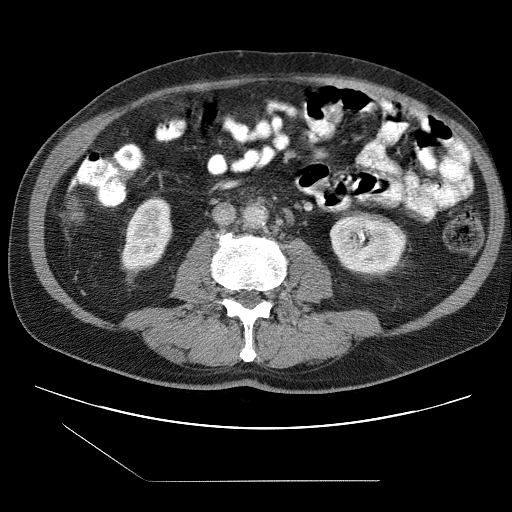
Contrast-enhanced abdominal CT (liver protocol), one axial slice. Position 7 of 109 along the scan axis. Reconstruction kernel STANDARD. One of 2 acquisitions stored at this slice position. Soft-tissue window (W 400 / L 40 HU). 2.5 mm slice thickness. 512 × 512 image matrix. Case-level facts recorded for this patient, not image findings: diagnosis: hepatocellular carcinoma (patient treated with transarterial chemoembolisation; whether this scan precedes or follows treatment is not stated here); TNM stage (as recorded): Stage-IIIB; Child-Pugh class: A; tumour nodularity: multinodular.
Outlined on this slice (semi-automatically segmented with operator editing):
- liver parenchyma outside the tumour (the mass and vessels are separate outlines, so this box may not span the whole liver): bounding box (x1, y1, x2, y2) in pixels: (73, 212, 81, 218)